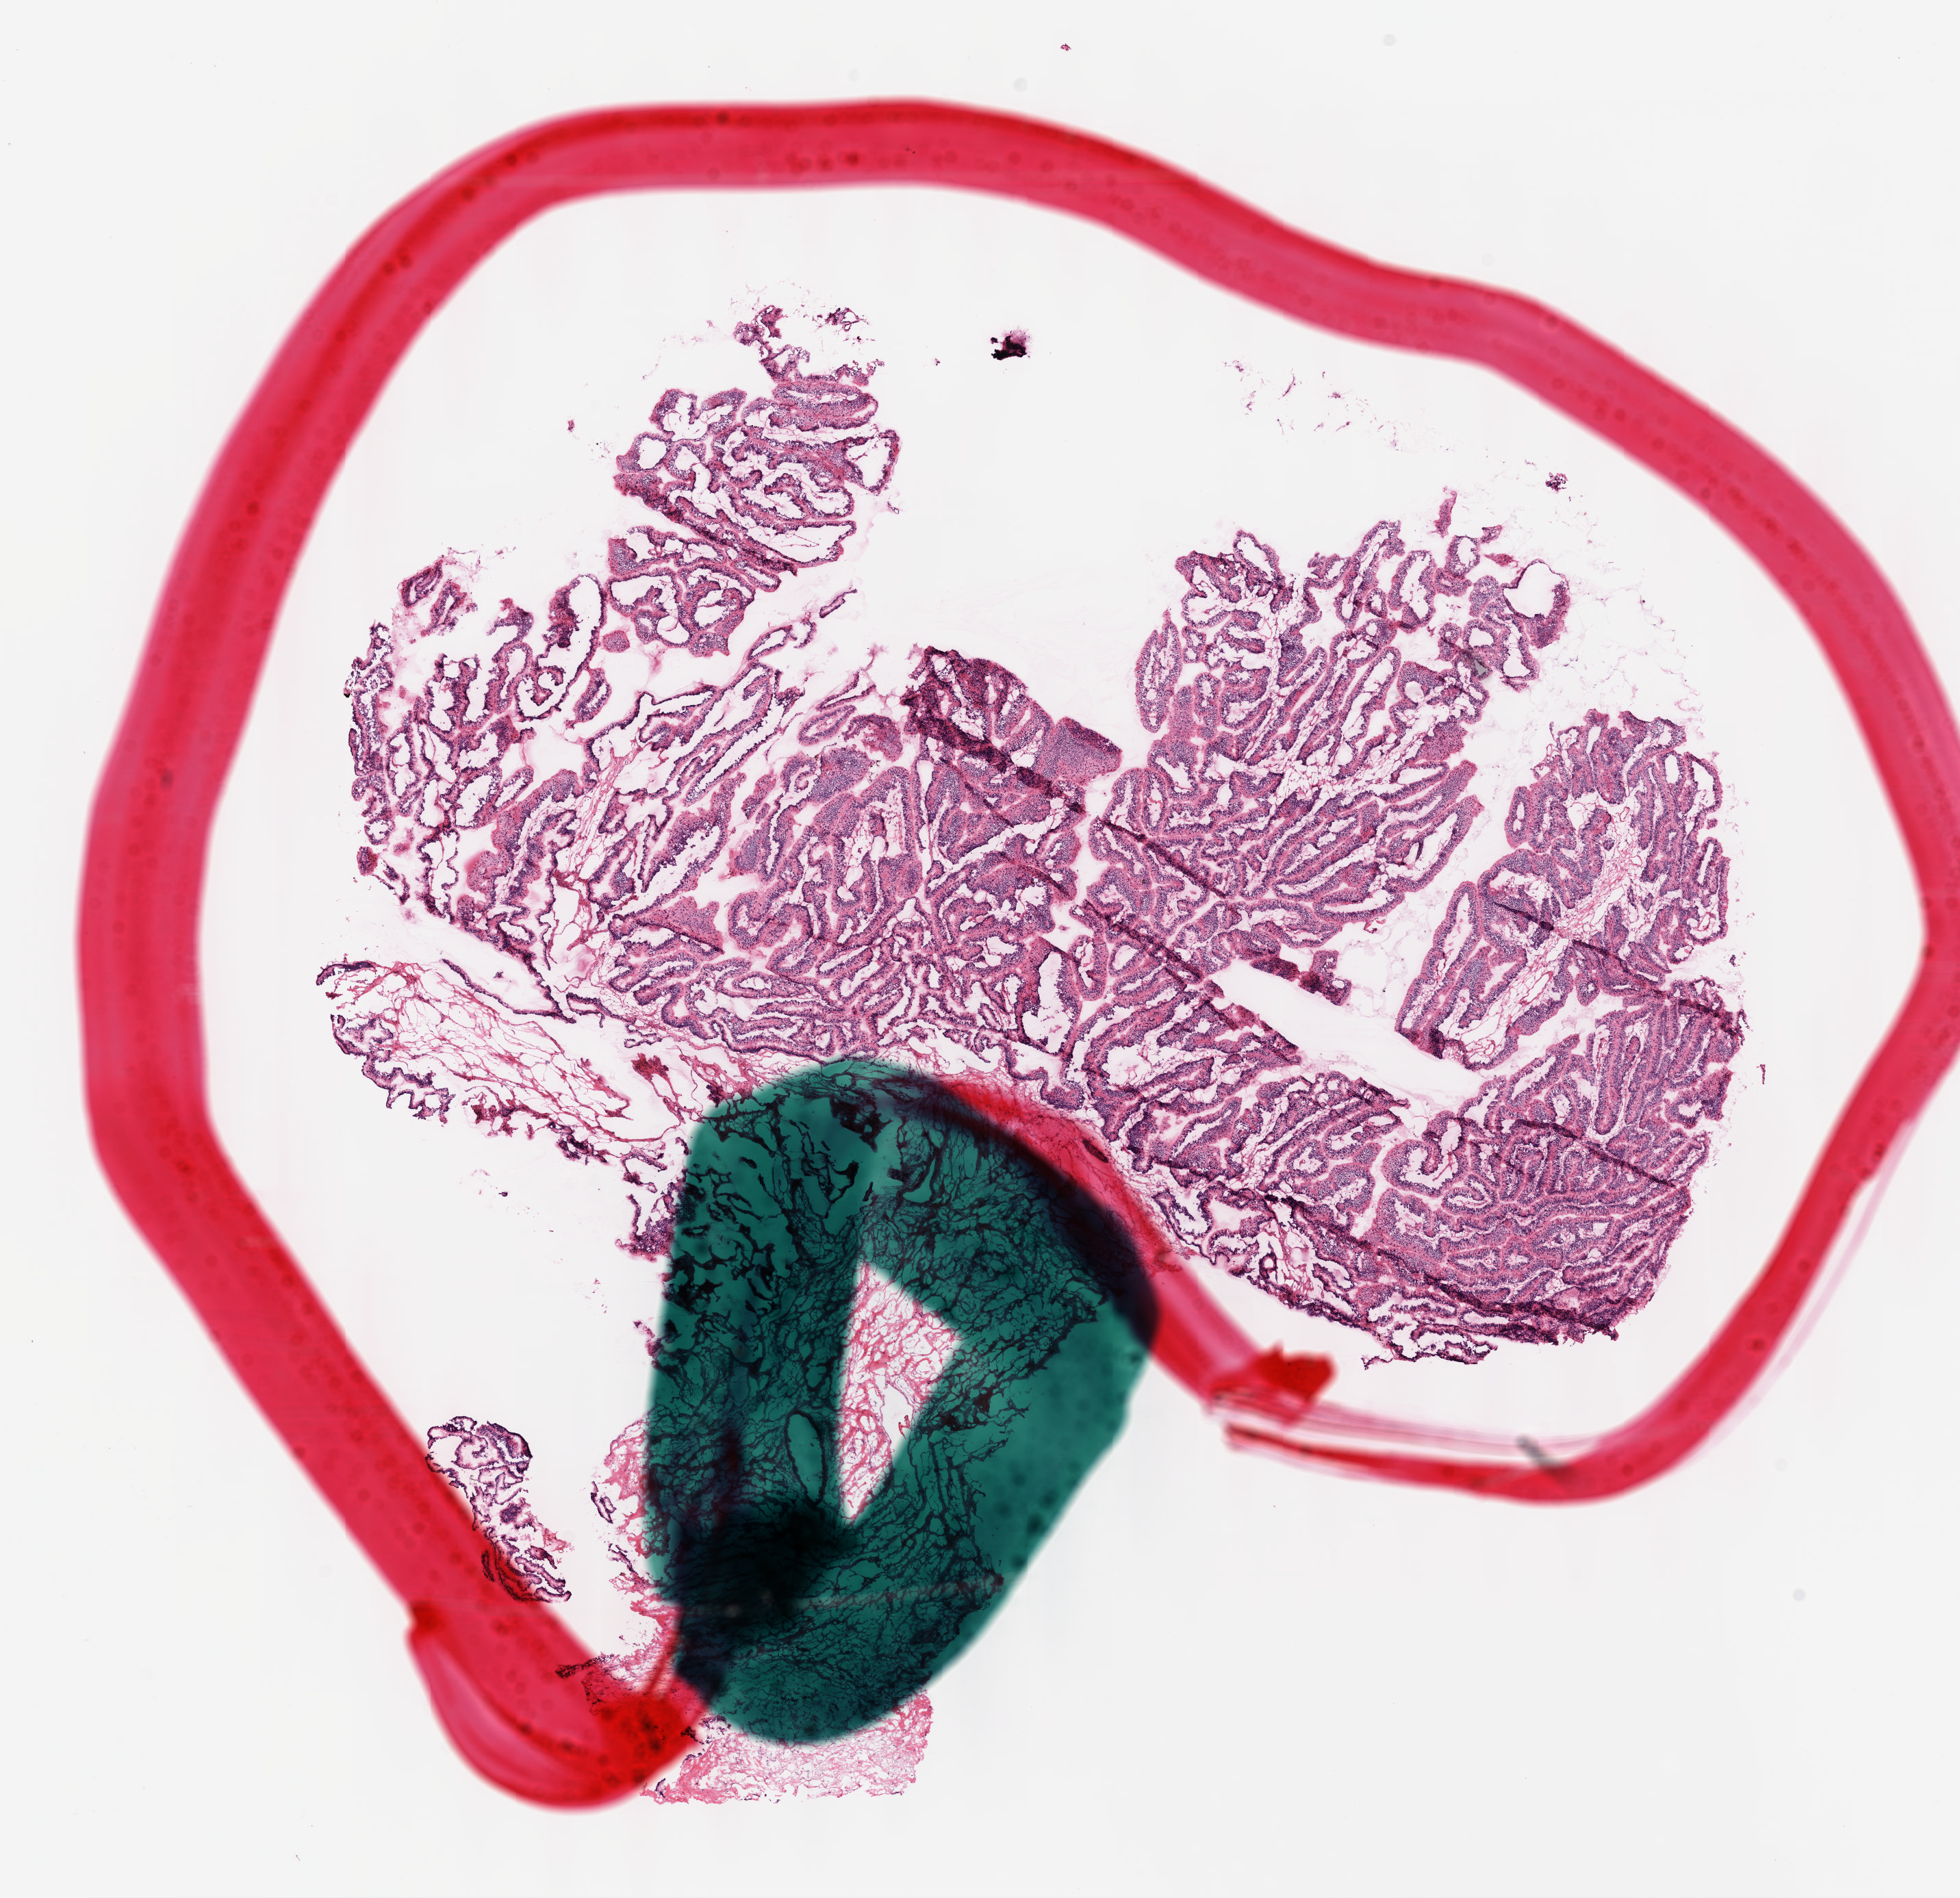
Whole-slide histology image, H&E-stained — low-resolution overview of the scanned area, about 11.6 x 11.2 mm, formalin-fixed paraffin-embedded (FFPE) diagnostic section, pancreas, primary tumour sample. Male patient; age at initial diagnosis 71 years. Histologic grade: G3 (poorly differentiated).
* AJCC pathologic stage: IIB (7th edition)
* lymph nodes positive (case pathology): 3 of 7 examined
* TNM: T3 N1 MX
* histologic diagnosis: Infiltrating duct carcinoma, NOS (head of pancreas)